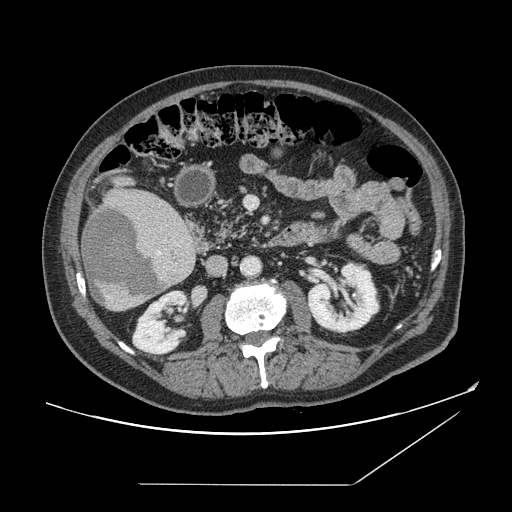
Contrast-enhanced abdominal CT, one axial slice. Position 61 of 166 along the scan axis. Intravenous contrast given. Soft-tissue window (W 400 / L 40 HU). 2.5 mm slice thickness. 512 × 512 image matrix, field of view 416 × 416 mm. Male patient, age 80 years. From the clinical record (not read from this slice): diagnosis: colorectal cancer liver metastases, imaged before liver resection; multiple liver metastases: no; largest metastasis: 2.2 cm; disease in both lobes: no.
Structures marked on this image (outlined manually by an expert reader):
- liver: box from (x=81, y=188) to (x=198, y=312) px
- planned liver remnant (the part of the liver to remain after resection): (x=131, y=190)–(x=169, y=209)
- liver metastasis: (x=82, y=206)–(x=166, y=304)